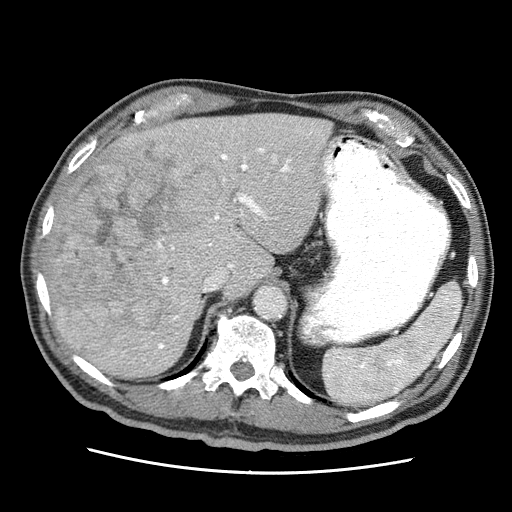
Contrast-enhanced abdominal CT (liver protocol), one axial slice. Position 40 of 75 along the scan axis. Reconstruction kernel STANDARD. Soft-tissue window (W 400 / L 40 HU). 2.5 mm slice thickness. 512 × 512 image matrix. From the clinical record (not read from this slice): diagnosis: hepatocellular carcinoma (patient treated with transarterial chemoembolisation; whether this scan precedes or follows treatment is not stated here); TNM stage (as recorded): Stage-IIIA; Child-Pugh class: A; tumour nodularity: multinodular; tumour size: 13.9 cm.
Annotated regions visible in this slice (semi-automatically segmented with operator editing):
- liver parenchyma outside the tumour (the mass and vessels are separate outlines, so this box may not span the whole liver): box from (x=48, y=114) to (x=332, y=378) px
- mass: (x=49, y=140)–(x=224, y=342)
- liver vessels: (x=122, y=120)–(x=321, y=360)